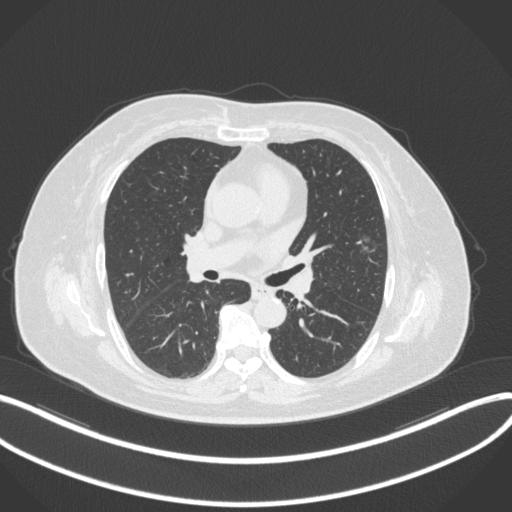
Chest CT, one axial slice. Slice 173 of 286 in the series (ordered by position). Reconstruction kernel B31f. Lung window (W 1500 / L -600 HU). 1 mm slice thickness. 512 × 512 image matrix. Patient: female, 76 years. Case-level facts recorded for this patient, not image findings: clinical TNM (as recorded): T1b N0 M0; histopathological grade: G1-2.
Outlined on this slice (bounding box drawn by a radiologist):
- lung tumour (recorded histology: adenocarcinoma): box from (x=352, y=223) to (x=381, y=261) px